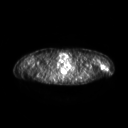
FDG PET of an extremity soft-tissue mass (from a PET/CT study), one axial slice. Position 201 of 267 along the scan axis. 3.27 mm slice thickness. 128 × 128 image matrix, field of view 600 × 600 mm. Patient: female, 28 years. Case-level facts recorded for this patient, not image findings: histological type: malignant fibrous histiocytoma; grade: low; site of the primary tumour: left arm.
Outlined on this slice (expert contour drawn on MRI and transferred to this co-registered scan by the dataset authors):
- gross tumour volume (mass): bounding box <100,63,106,69> (left, top, right, bottom; pixels)